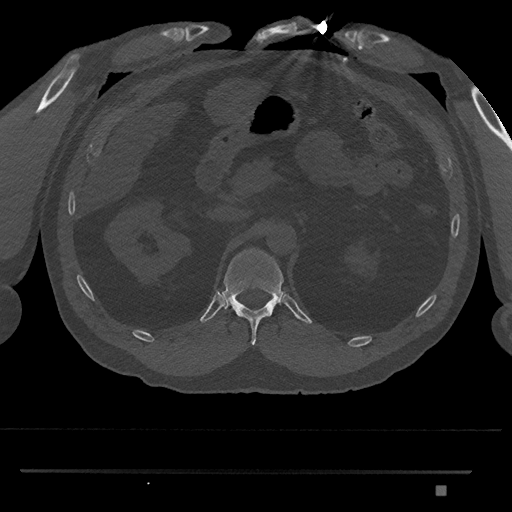
CT including the spine, one axial slice; slice 882 of 1134 in the series (ordered by position); reconstruction kernel Br40s/3; bone window (W 1800 / L 400 HU); 0.5 mm slice thickness; 512 × 512 image matrix, field of view 429 × 429 mm. Patient: male, 65 years. Case-level facts recorded for this patient, not image findings: primary cancer: prostate.
Outlined on this slice (semi-automatically segmented with operator editing):
- T12 vertebra: bounding box [x1, y1, x2, y2] px = [219, 248, 285, 346]